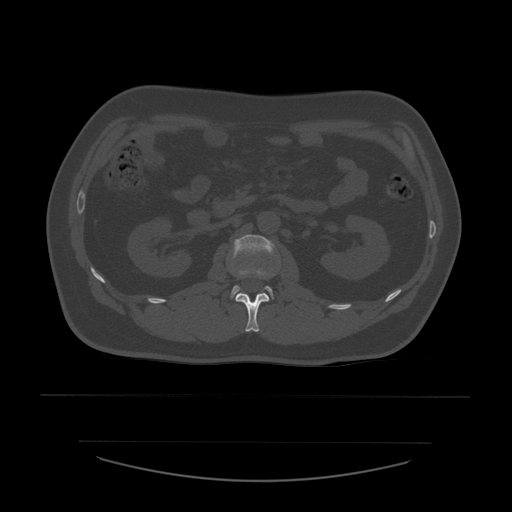
CT including the spine, one axial slice; position 215 of 532 along the scan axis; 120 kVp; bone window (W 1800 / L 400 HU); 512 × 512 image matrix, field of view 441 × 441 mm. Patient age 44 years. Case-level facts recorded for this patient, not image findings: primary cancer: soft tissue sarcoma.
Annotated regions visible in this slice (semi-automatic segmentation, software-assisted and operator-edited):
- L1 vertebra: bounding box [x1, y1, x2, y2] px = [236, 276, 270, 332]
- L2 vertebra: [231, 235, 274, 299]